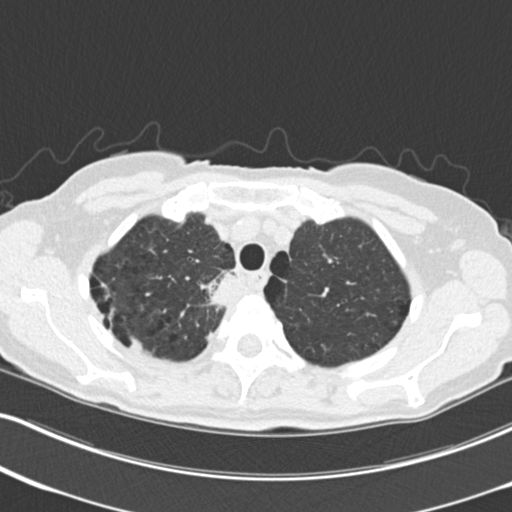
Chest CT (low-dose screening protocol), one axial image. Third screening round (two years after baseline). Lung window (W 1500 / L -600 HU). 2 mm slice thickness. Female, age 68 years at enrolment. Current smoker at enrolment.
Expert reader's lesion annotation, bounding box <200,263,251,318> (left, top, right, bottom; pixels). Reader record for this screening exam (exam-level; its link to the box is not recorded): non-calcified nodule or mass ≥4 mm, right upper lobe, 31 × 29 mm, poorly defined margins, soft tissue attenuation, pre-existing on the prior screen: no. Official screen result: positive, other. Later outcome: lung cancer diagnosed 79 days after this screen — squamous cell carcinoma, NOS, right upper lobe, mediastinum, poorly differentiated (G3), stage IIIB (AJCC 6th edition), 43 mm at pathology.